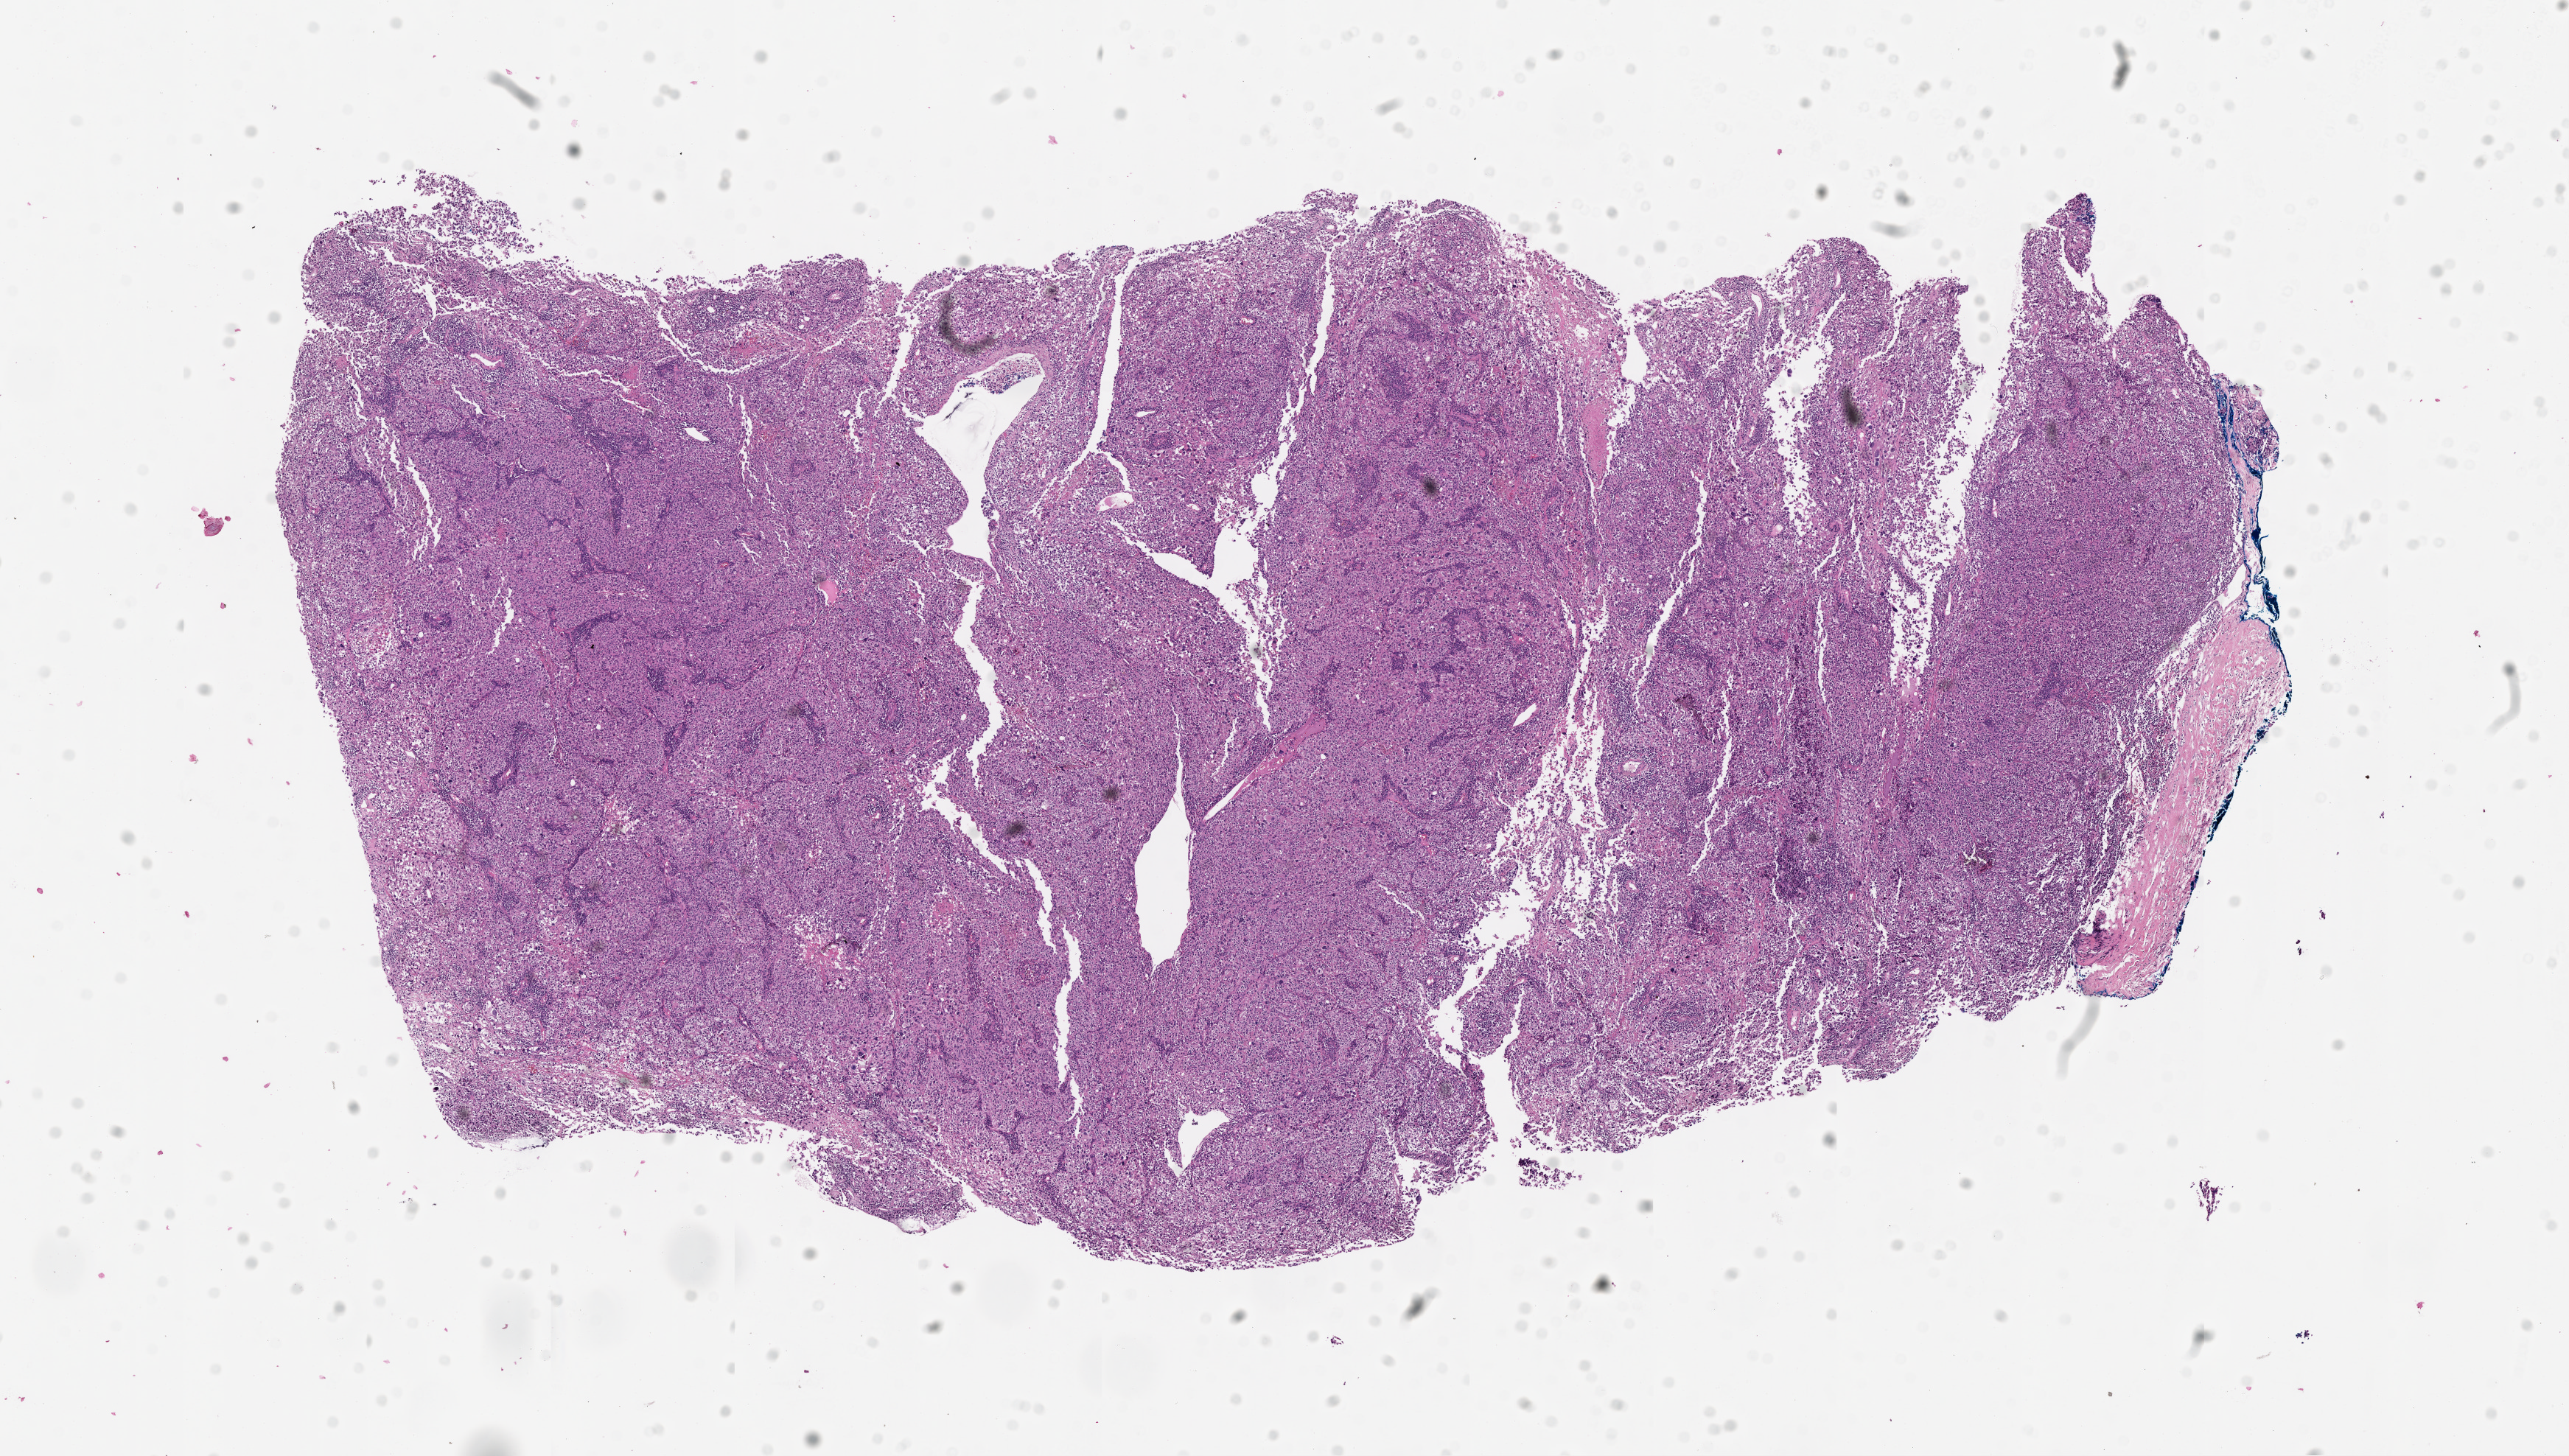
Digitized Hematoxylin and eosin (H&E) stained tissue section (whole slide), whole scanned area (about 14.0 x 8.0 mm, slide scanned at 20x) shown as a low-resolution overview. Tumour tissue sample, sampled site: lymph node. 54-year-old female patient. Pathologist review of this section (percent, as recorded): tumour nuclei 80%, necrosis 0%.
This section: metastatic tumour tissue. Patient diagnosis: Malignant melanoma, NOS.